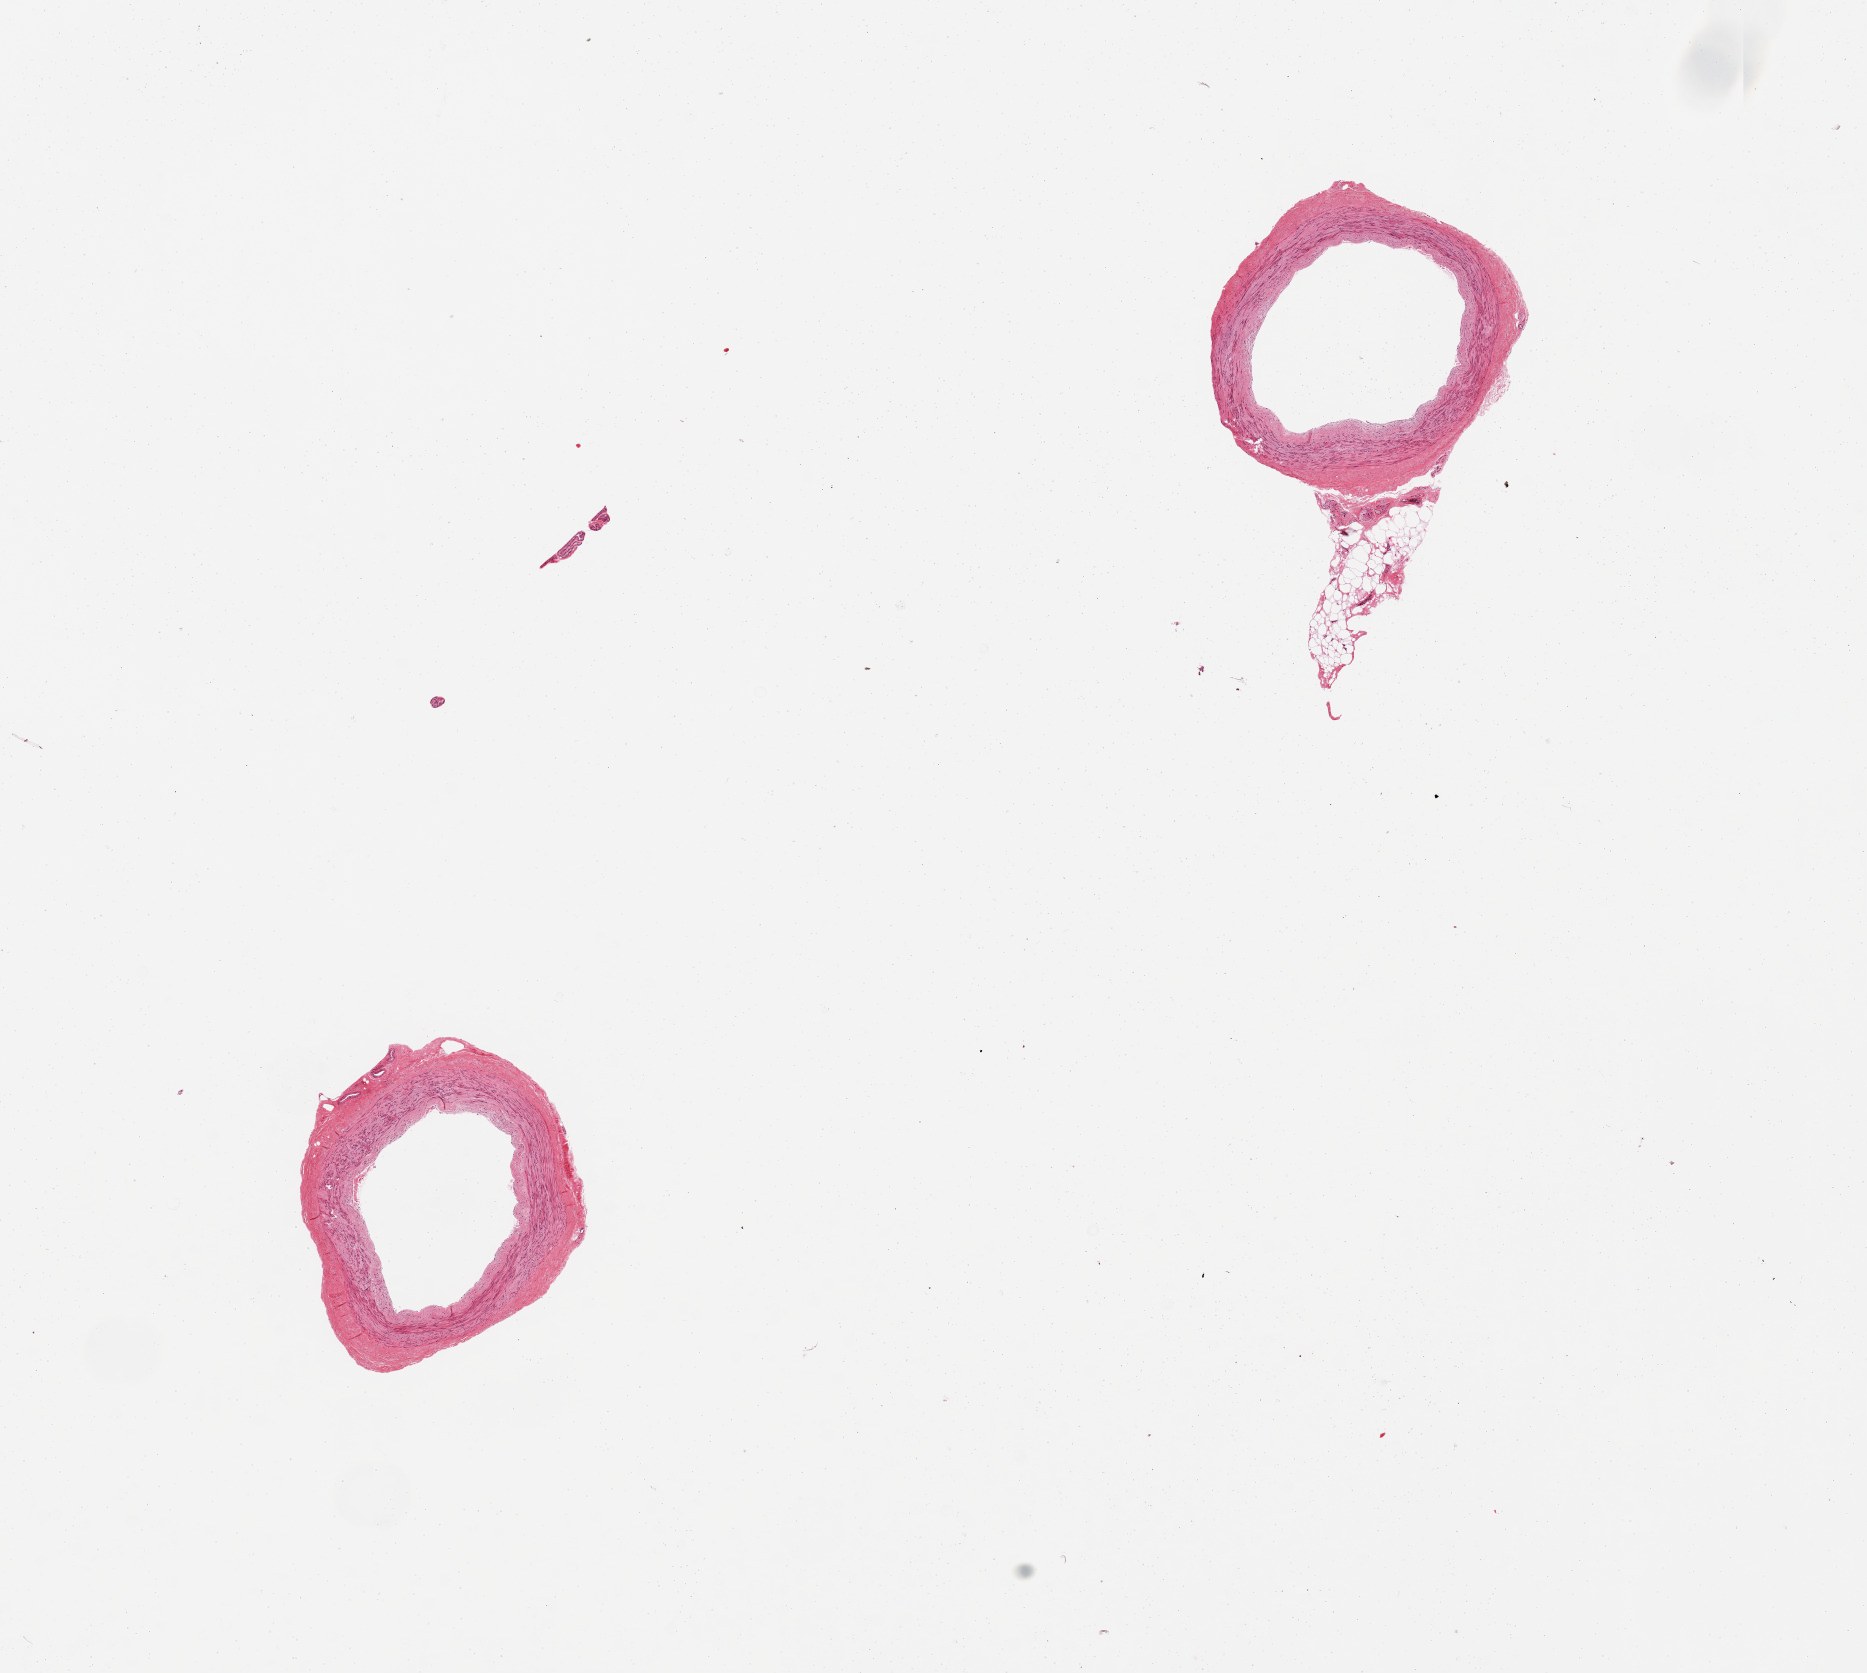
Hematoxylin and eosin (H&E) whole-slide image, a low-resolution overview of the entire scanned area, about 14.8 x 13.2 mm (slide scanned at 20x).
* specimen: PAXgene-fixed, paraffin-embedded tissue; target tissue: tibial artery; tissue donor sample